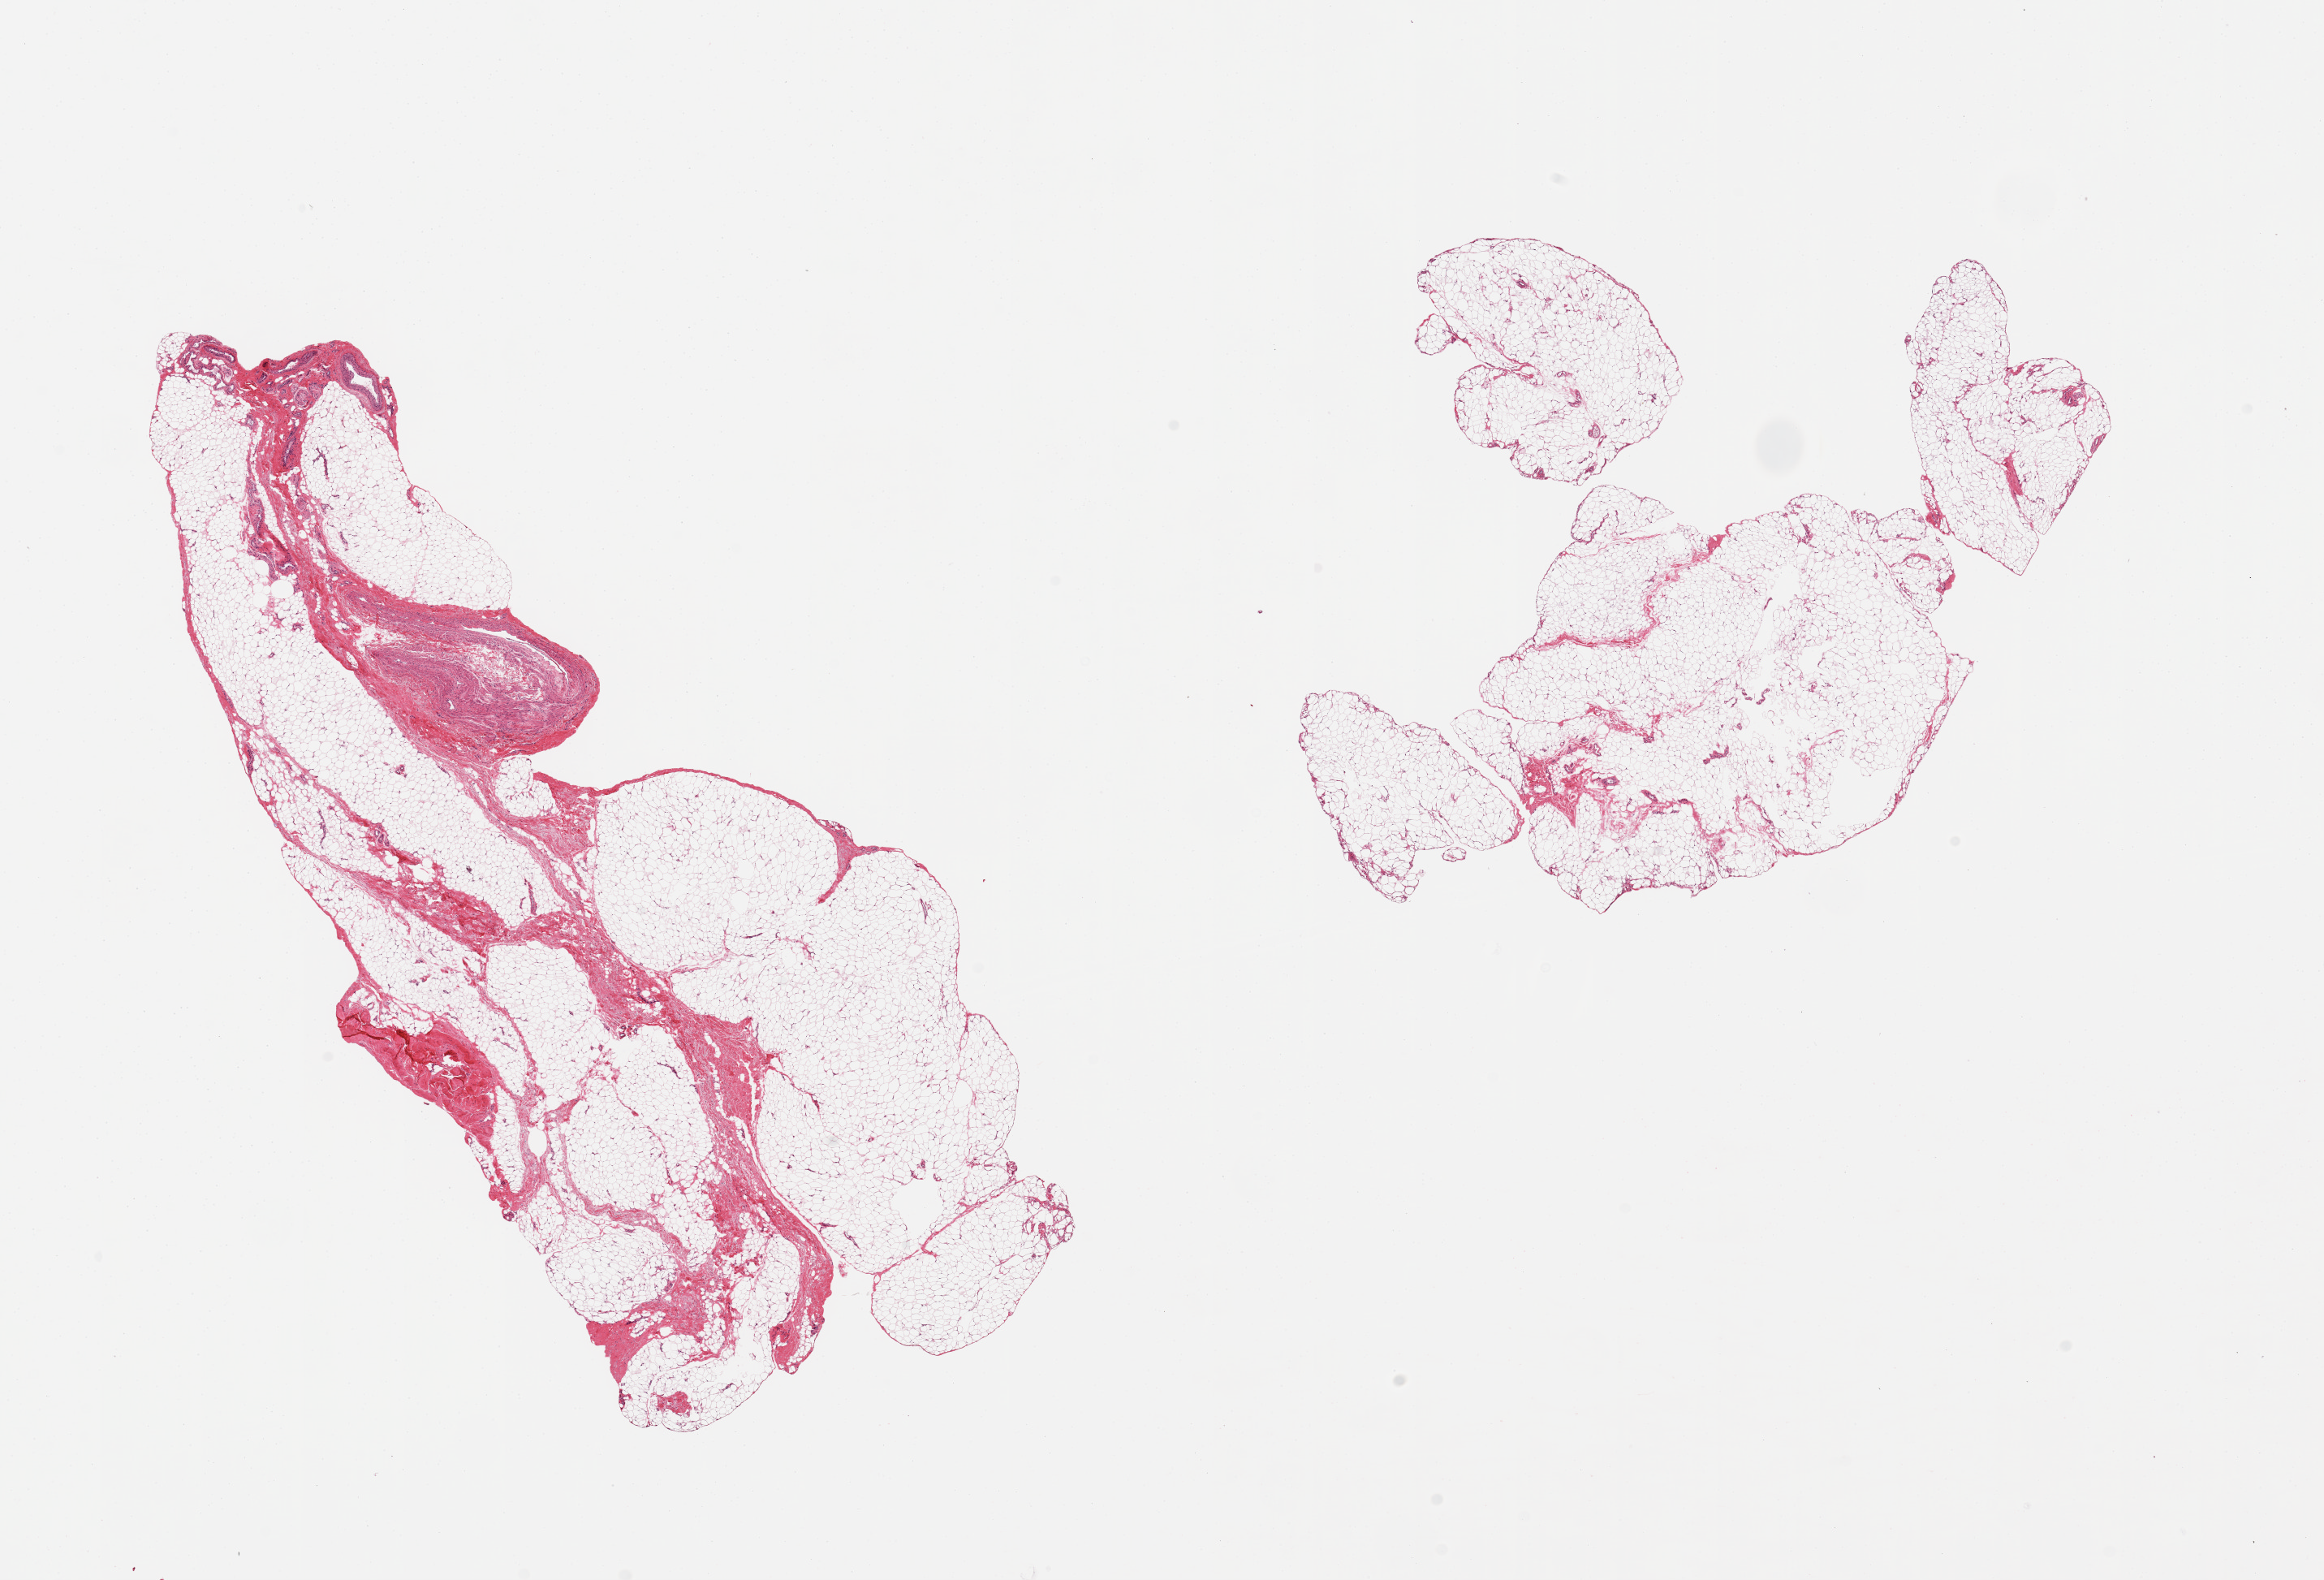
Digitized haematoxylin and eosin-stained section — a low-resolution overview of the entire scanned area, about 22.6 x 15.4 mm. PAXgene-fixed paraffin-embedded (PFPE) section. Sampled site (target tissue): adipose tissue. Tissue donor sample.
• pathologist's review note for this sample: 2 pieces; one piece is ~25% fibrous/vascular tissue